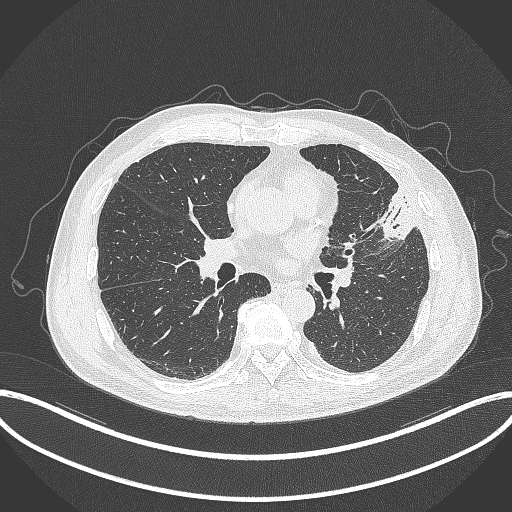
Chest CT, one axial slice. Position 168 of 382 along the scan axis. 120 kVp. Lung window (W 1500 / L -600 HU). 1 mm slice thickness. 512 × 512 image matrix, field of view 415 × 415 mm. Male patient, age 64 years. From the clinical record (not read from this slice): clinical TNM (as recorded): T4 N1 M0; histopathological grade: G3.
Outlined on this slice (rectangle marked by the reading radiologist):
- lung tumour (recorded histology: adenocarcinoma): box from (x=373, y=186) to (x=415, y=243) px